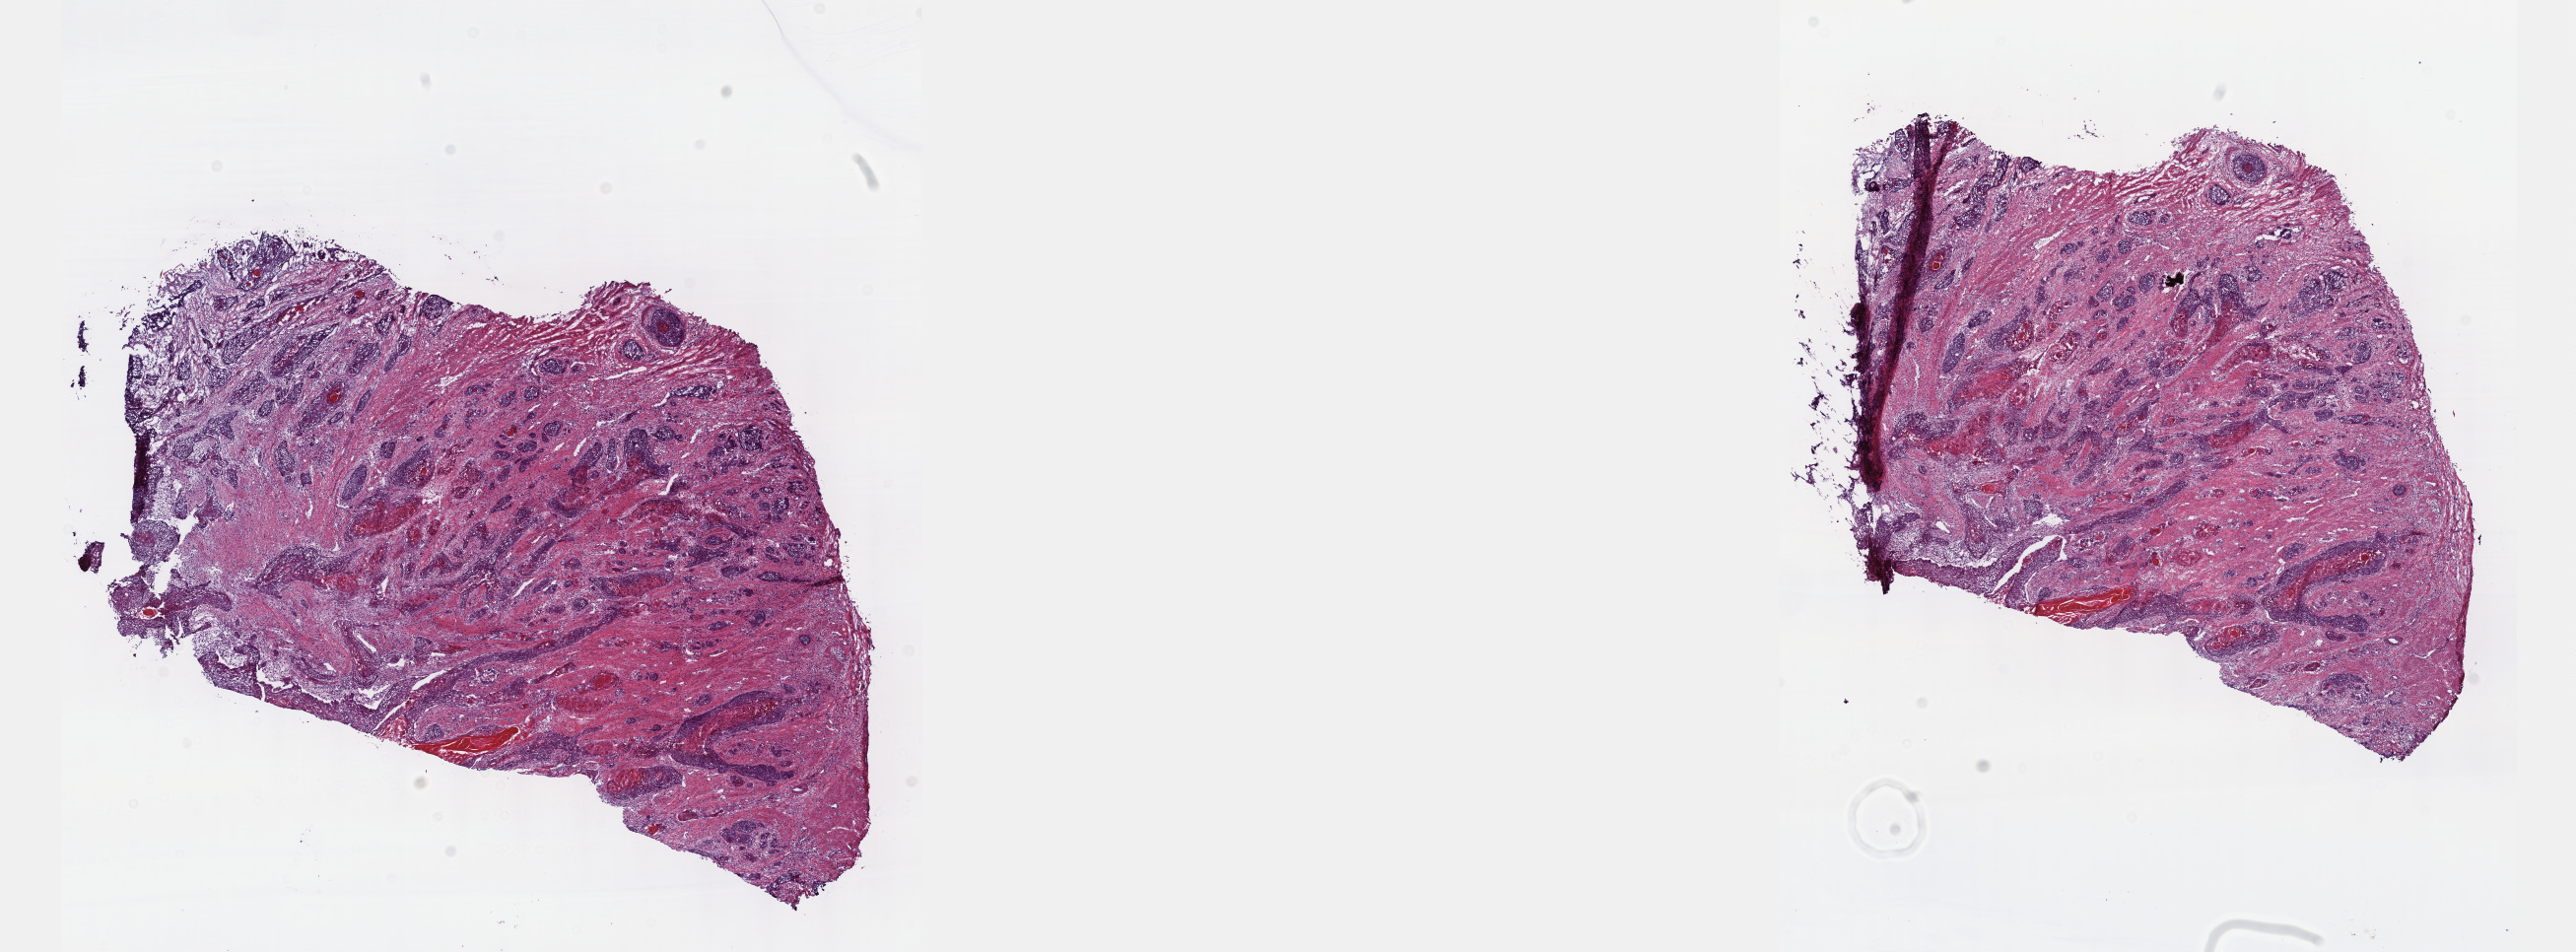
Hematoxylin and eosin (H&E) stained whole-slide image — a low-resolution overview of the entire scanned area, about 21.1 x 7.8 mm, frozen section, esophagus, primary tumour sample. Male, age 58 years at initial diagnosis. Histologic grade: G2 (moderately differentiated). Pathologist review of this section (percent, as recorded): tumour cells 25%, tumour nuclei 65%, normal cells 0%, stromal cells 65%, necrosis 10%. Infiltration values recorded for this section: lymphocyte infiltration 4%, monocyte infiltration 1%, neutrophil infiltration 1%.
• TNM: T2 N0 M0
• lymph nodes positive (case pathology): 0 of 4 examined
• histologic diagnosis: Squamous cell carcinoma, NOS (lower third of esophagus)
• AJCC pathologic stage: IIA